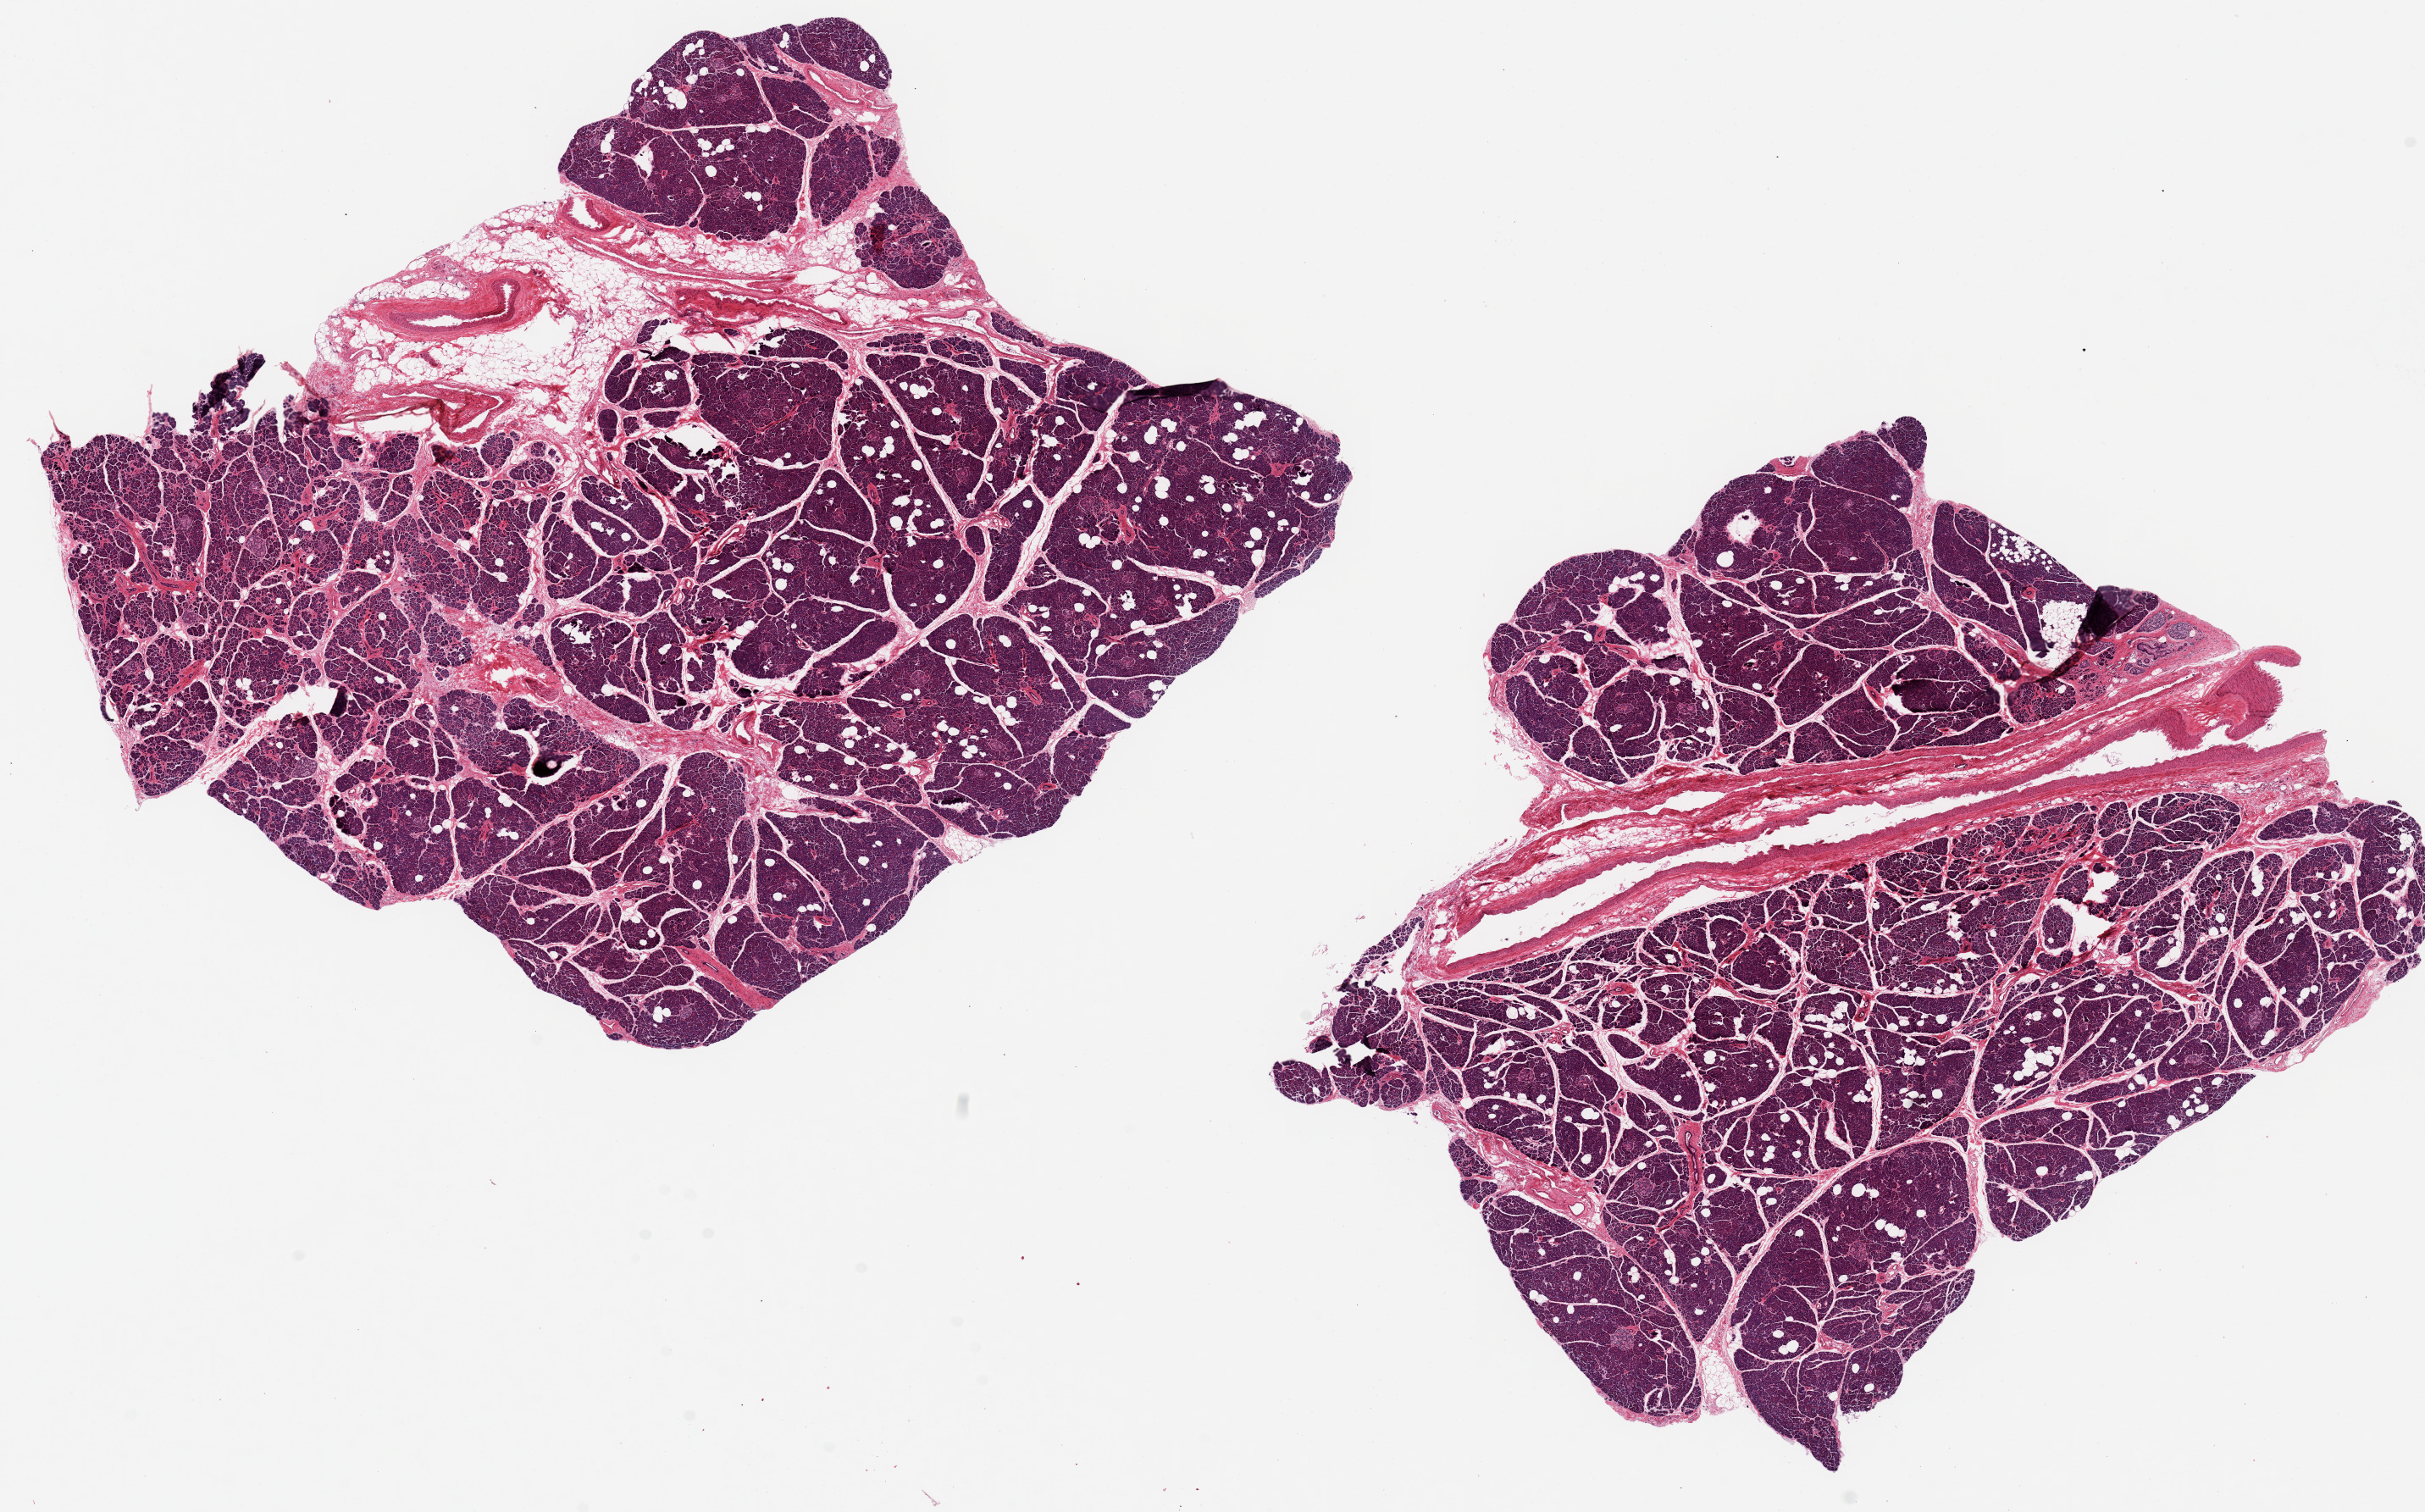
Whole-slide image, hematoxylin and eosin (H&E) stain — shown as a low-resolution overview of the whole scanned area (about 22.6 x 14.1 mm, slide scanned at 20x); PAXgene-fixed paraffin-embedded (PFPE) section; target tissue: pancreas; tissue donor sample. Donor: female.
Reviewer comment on this tissue sample: 2 pieces, 10x9 & 9x8mm; ~10 interstitial fat/vessels; Islets well preserved.